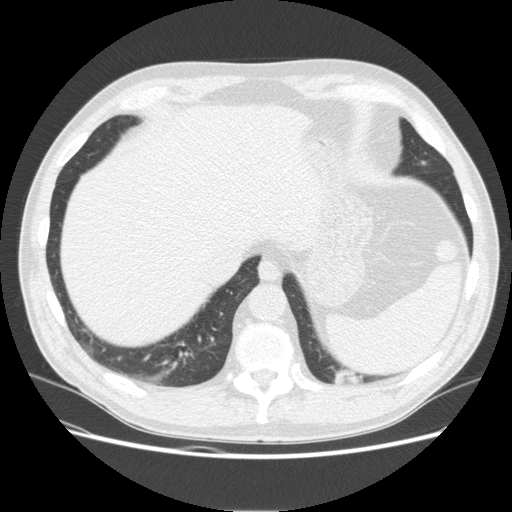
Low-dose screening chest CT, one axial slice; position 42 of 165 along the scan axis; reconstruction kernel STANDARD; 120 kVp; lung window (W 1500 / L -600 HU); 2.5 mm slice thickness; 512 × 512 image matrix.
Outlined on this slice (manually delineated by an expert):
- lesion 1 (tumor, upper lobe of left lung): bounding box (x1, y1, x2, y2) in pixels: (334, 368, 360, 385)